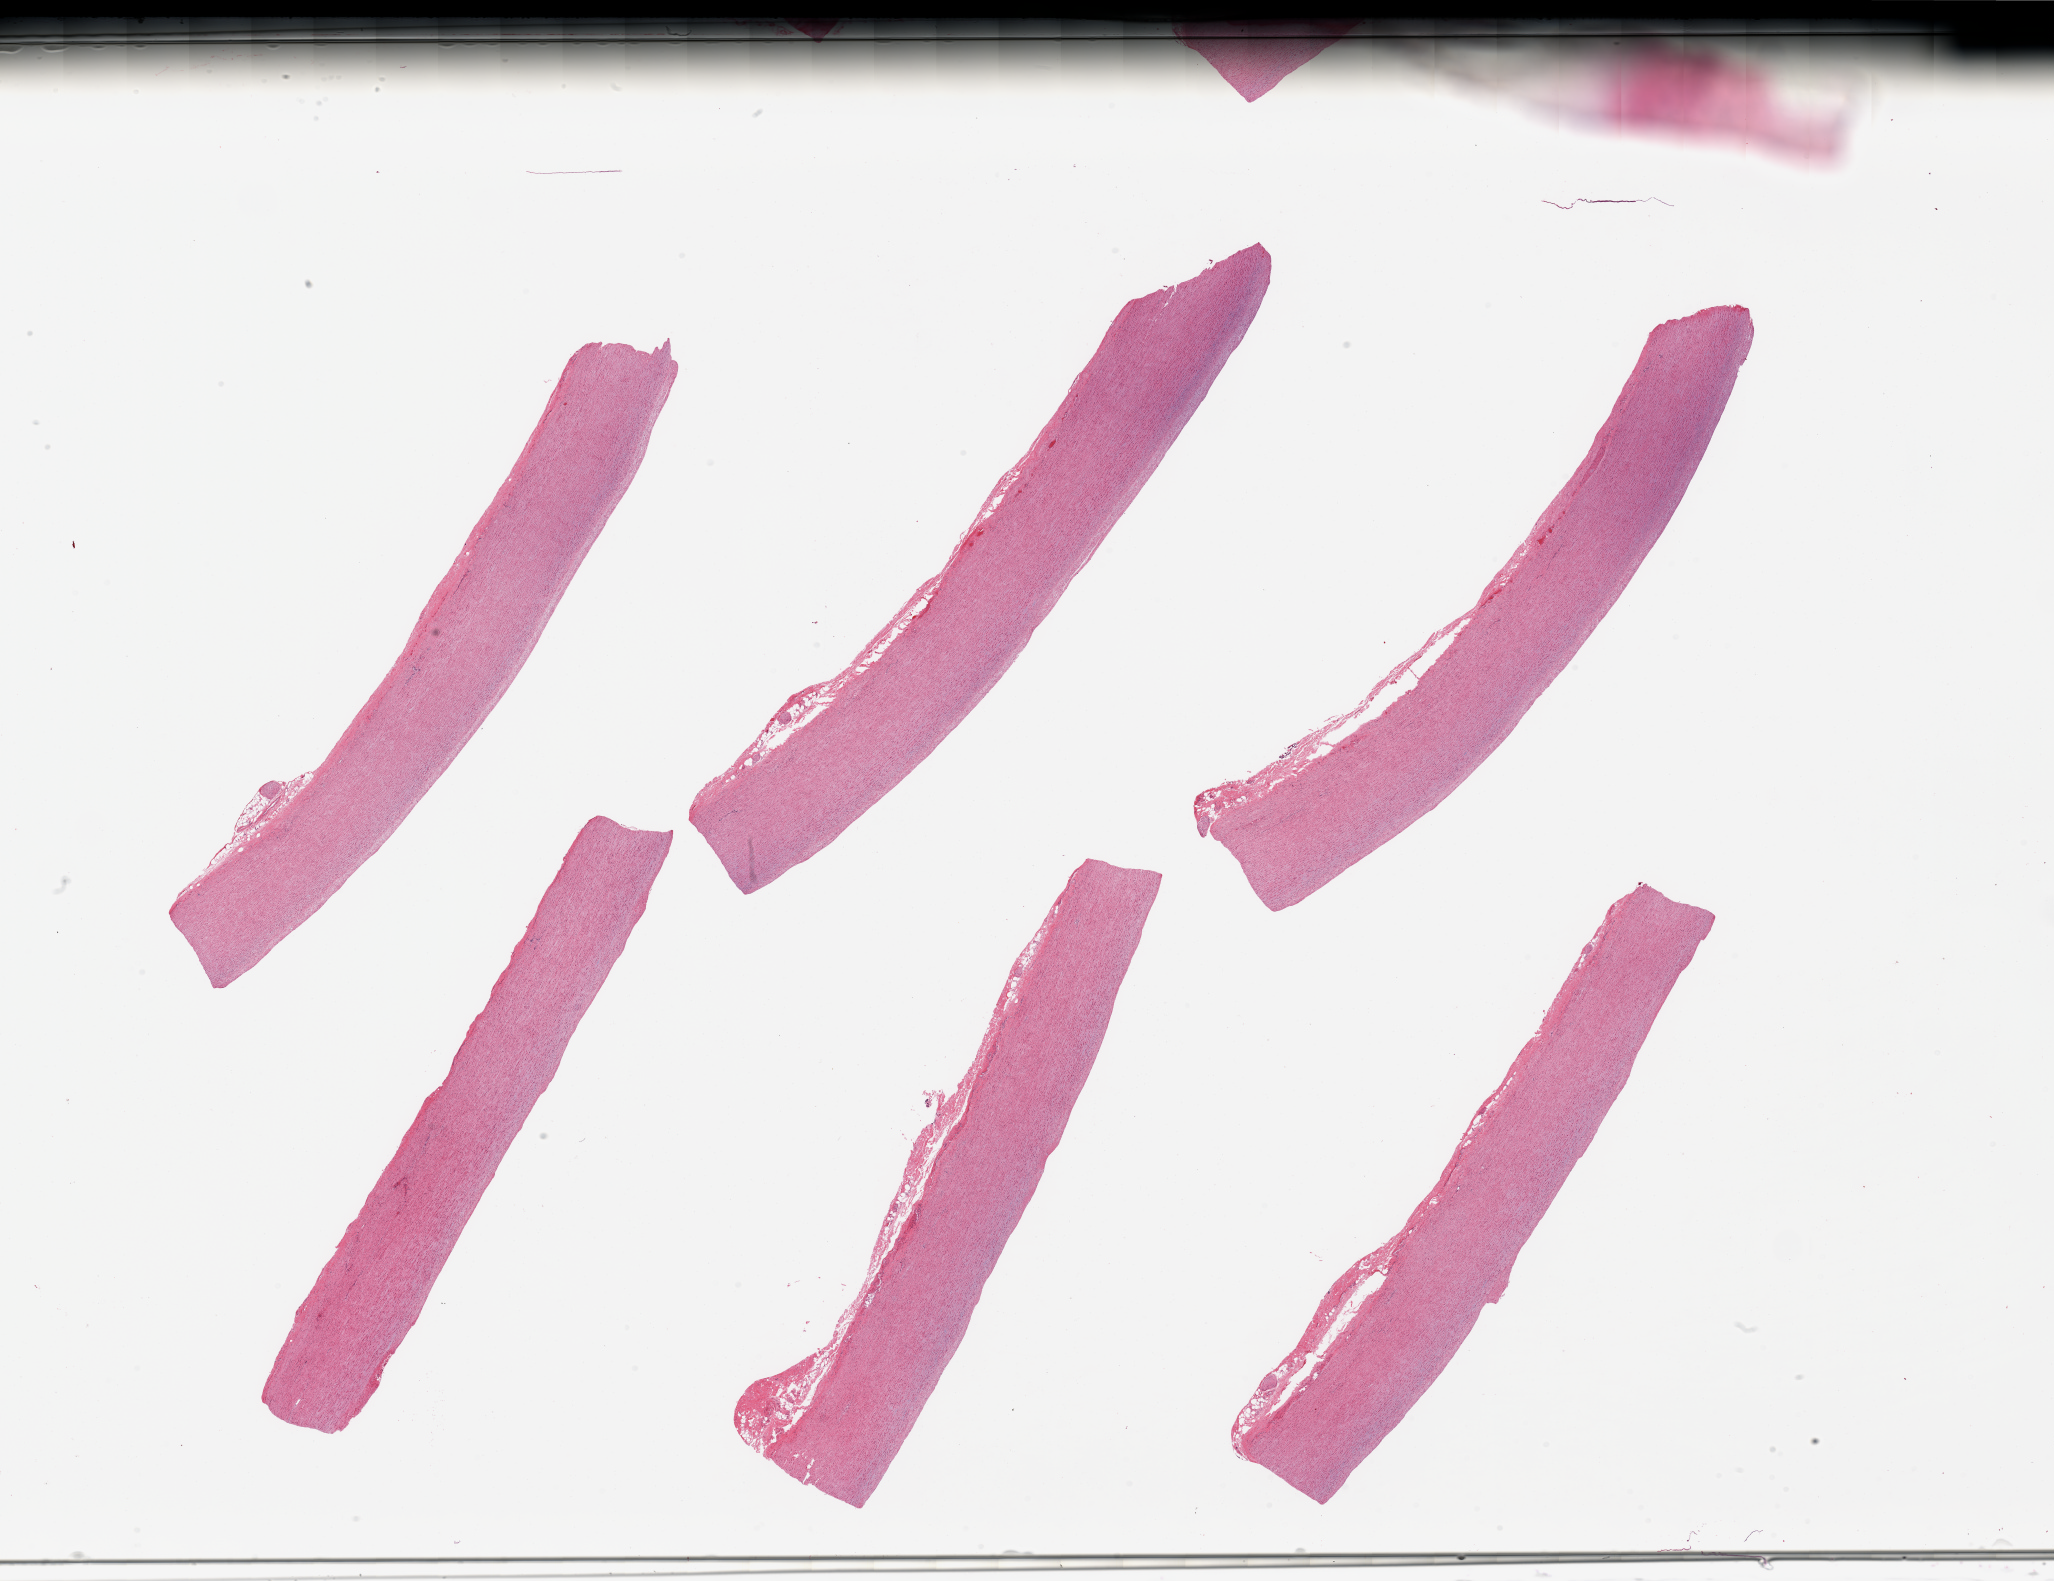
Digitized hematoxylin and eosin (H&E)-stained section, a low-resolution overview of the entire scanned area, about 32.5 x 25.0 mm (acquisition: 20x scan), PAXgene-fixed, paraffin-embedded tissue, sampled site (target tissue): aorta, tissue donor sample.
Reviewer comment on this tissue sample: 6 pieces; well trimmed; plaque free.